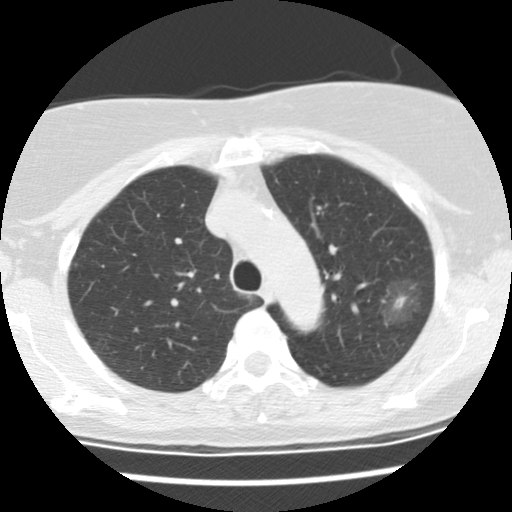
Low-dose screening chest CT, one axial slice; position 106 of 137 along the scan axis; reconstruction kernel STANDARD; lung window (W 1500 / L -600 HU); 2.5 mm slice thickness; 512 × 512 image matrix, field of view 288 × 288 mm.
Structures marked on this image (outlined manually by an expert reader):
- lesion 1 (tumor, upper lobe of left lung): box from (x=393, y=293) to (x=409, y=312) px